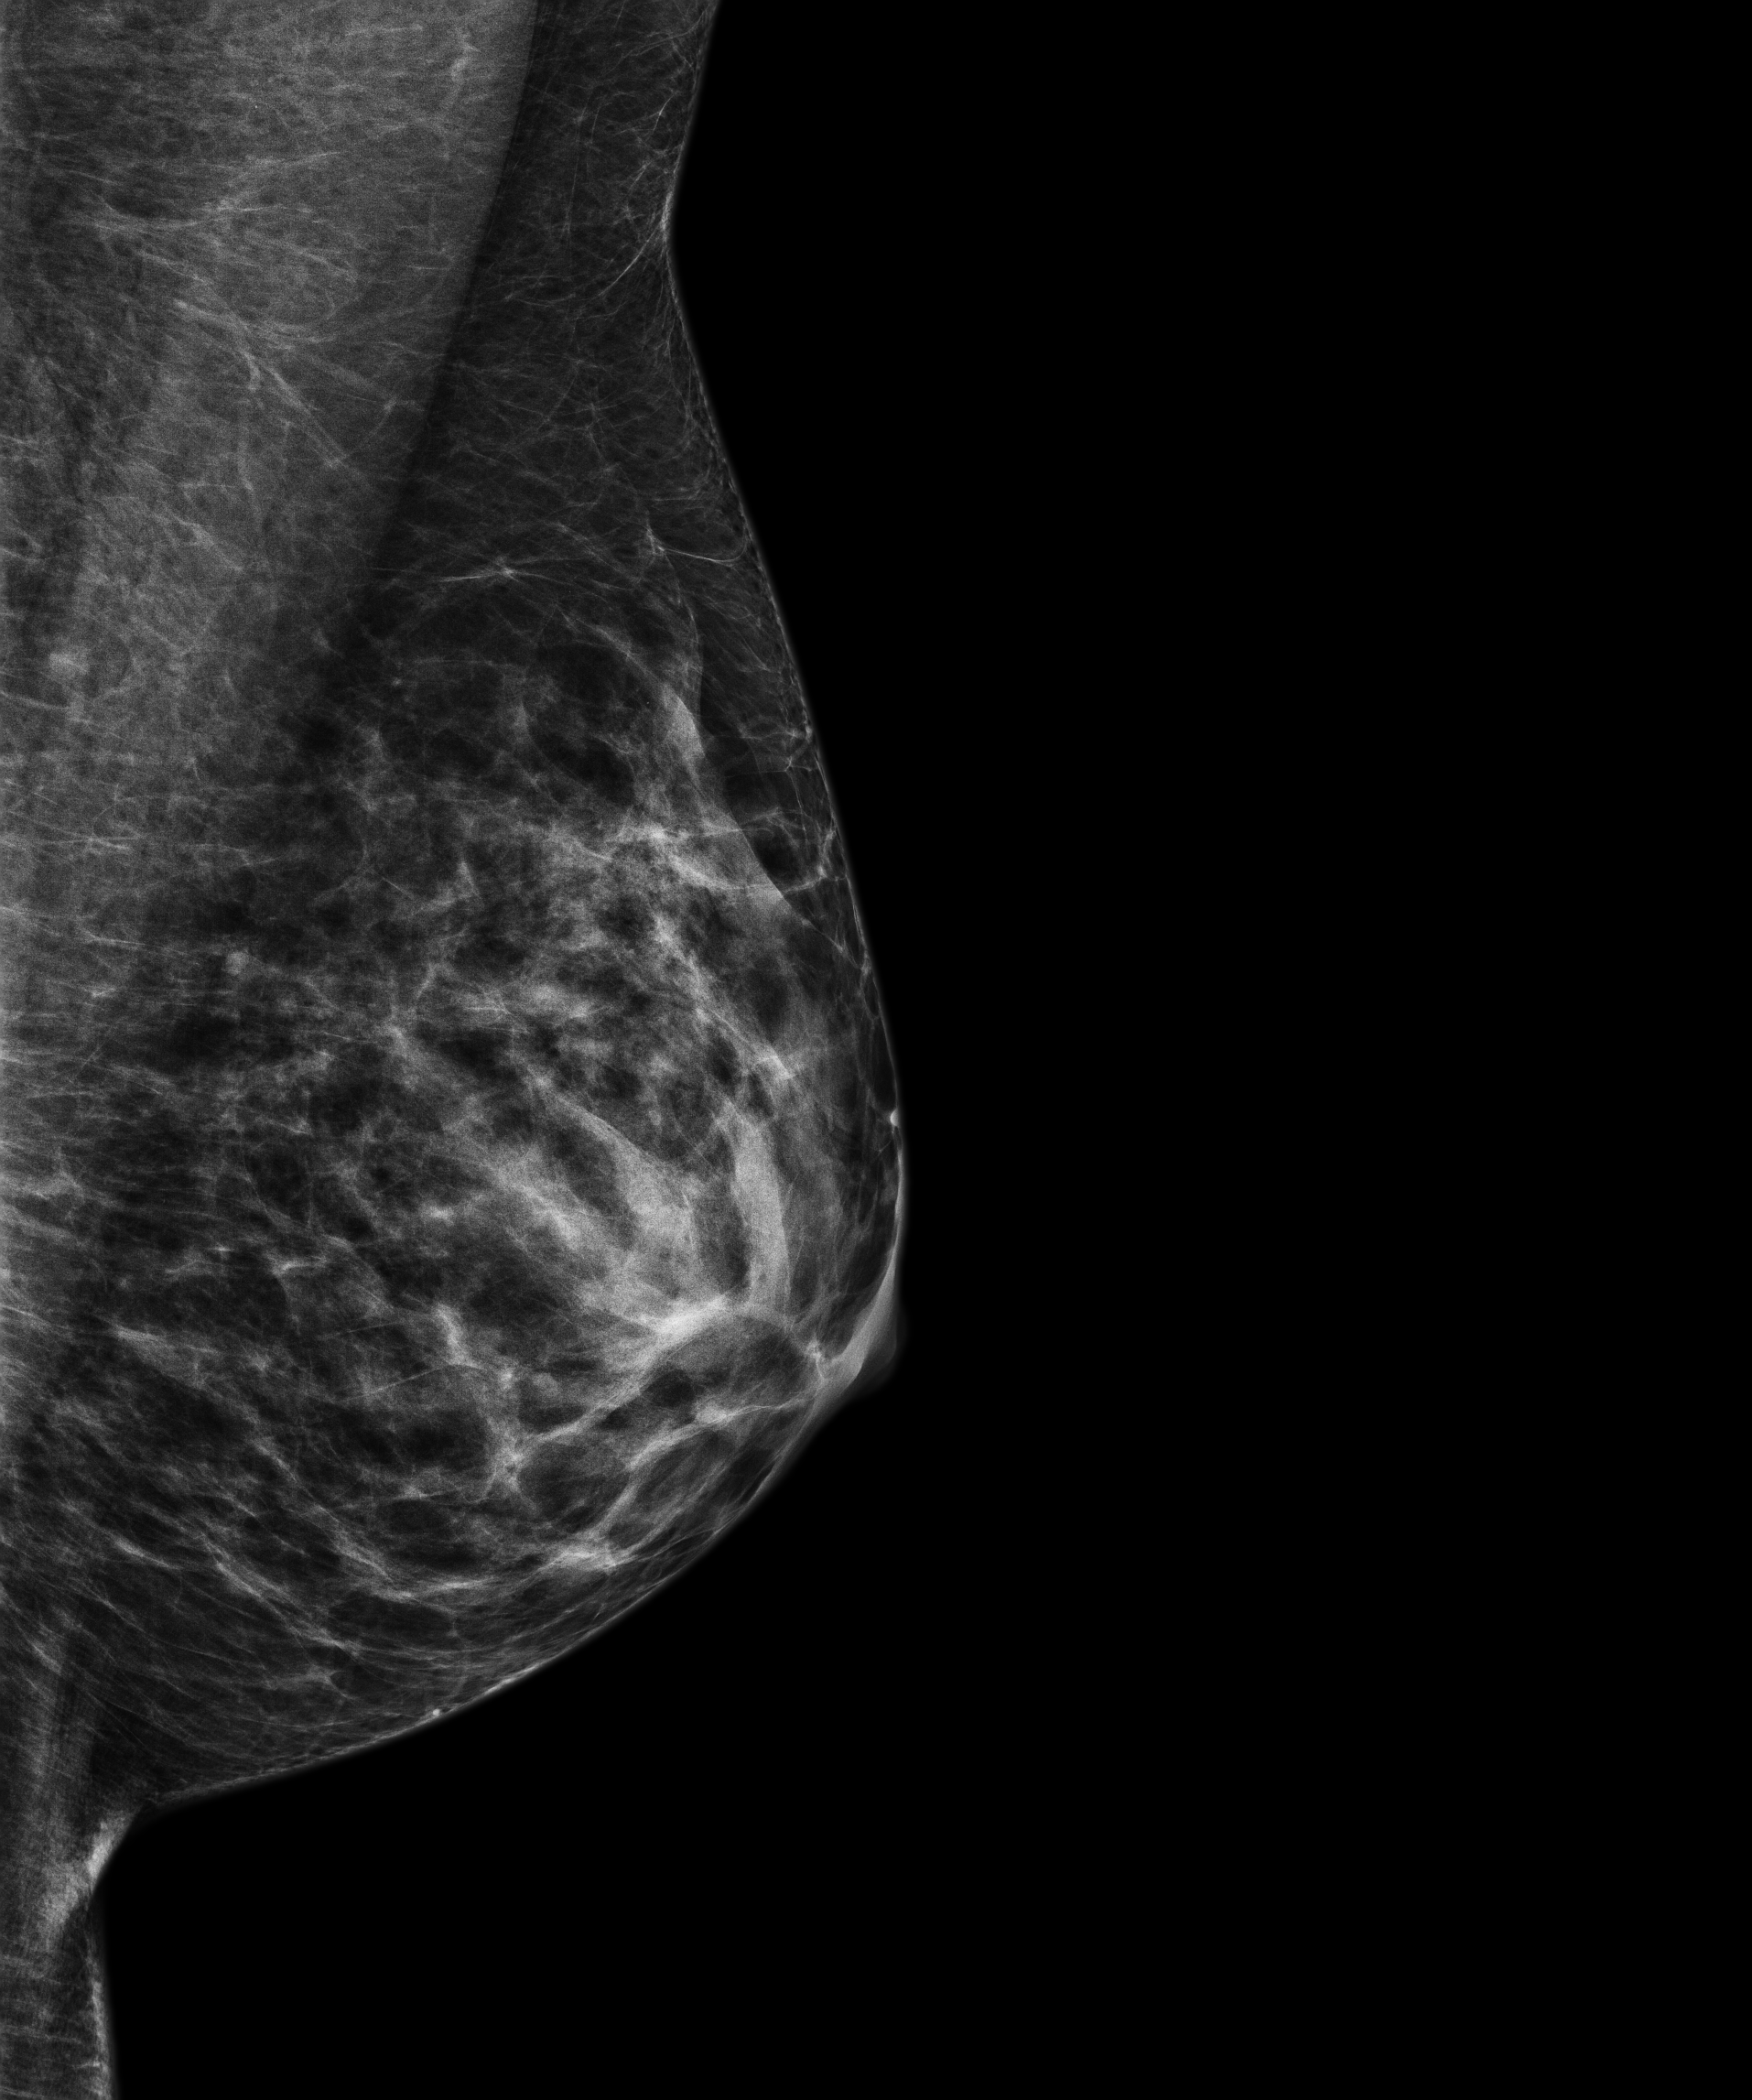
Annual screening mammography examination; compressed breast thickness 46 mm; system: Senographe Pristina. Female patient, age 43 years.
Image type: full-field digital mammogram. Breast: left. Projection: MLO view.